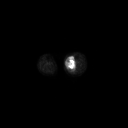
FDG PET of an extremity soft-tissue mass (from a PET/CT study), one axial slice; position 140 of 223 along the scan axis; 128 × 128 image matrix, field of view 700 × 700 mm. Patient: female, 70 years. From the clinical record (not read from this slice): histological type: extraskeletal high grade osteogenic sarcoma; grade: high; site of the primary tumour: left calf.
Outlined on this slice (expert contour drawn on MRI and transferred to this co-registered scan by the dataset authors):
- gross tumour volume (mass): bounding box (x1, y1, x2, y2) in pixels: (66, 58, 76, 70)